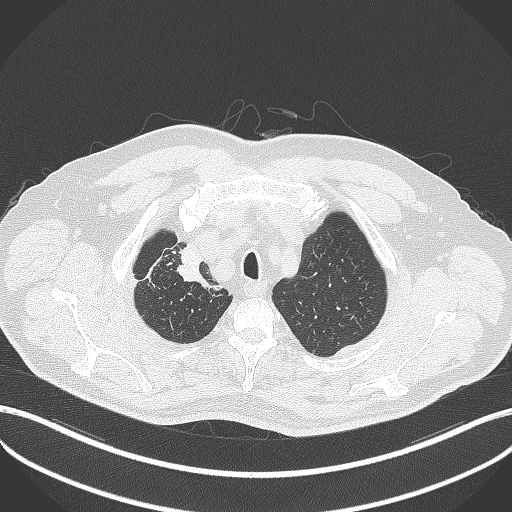
Chest CT, one axial slice. Slice 333 of 411 in the series (ordered by position). Reconstruction kernel B70f. 120 kVp. Lung window (W 1500 / L -600 HU). 512 × 512 image matrix. Male patient, age 60 years. Case-level facts recorded for this patient, not image findings: clinical TNM (as recorded): T1b N1 M0.
Outlined on this slice (rectangle marked by the reading radiologist):
- lung tumour (recorded histology: squamous cell carcinoma): bounding box <177,239,218,290> (left, top, right, bottom; pixels)